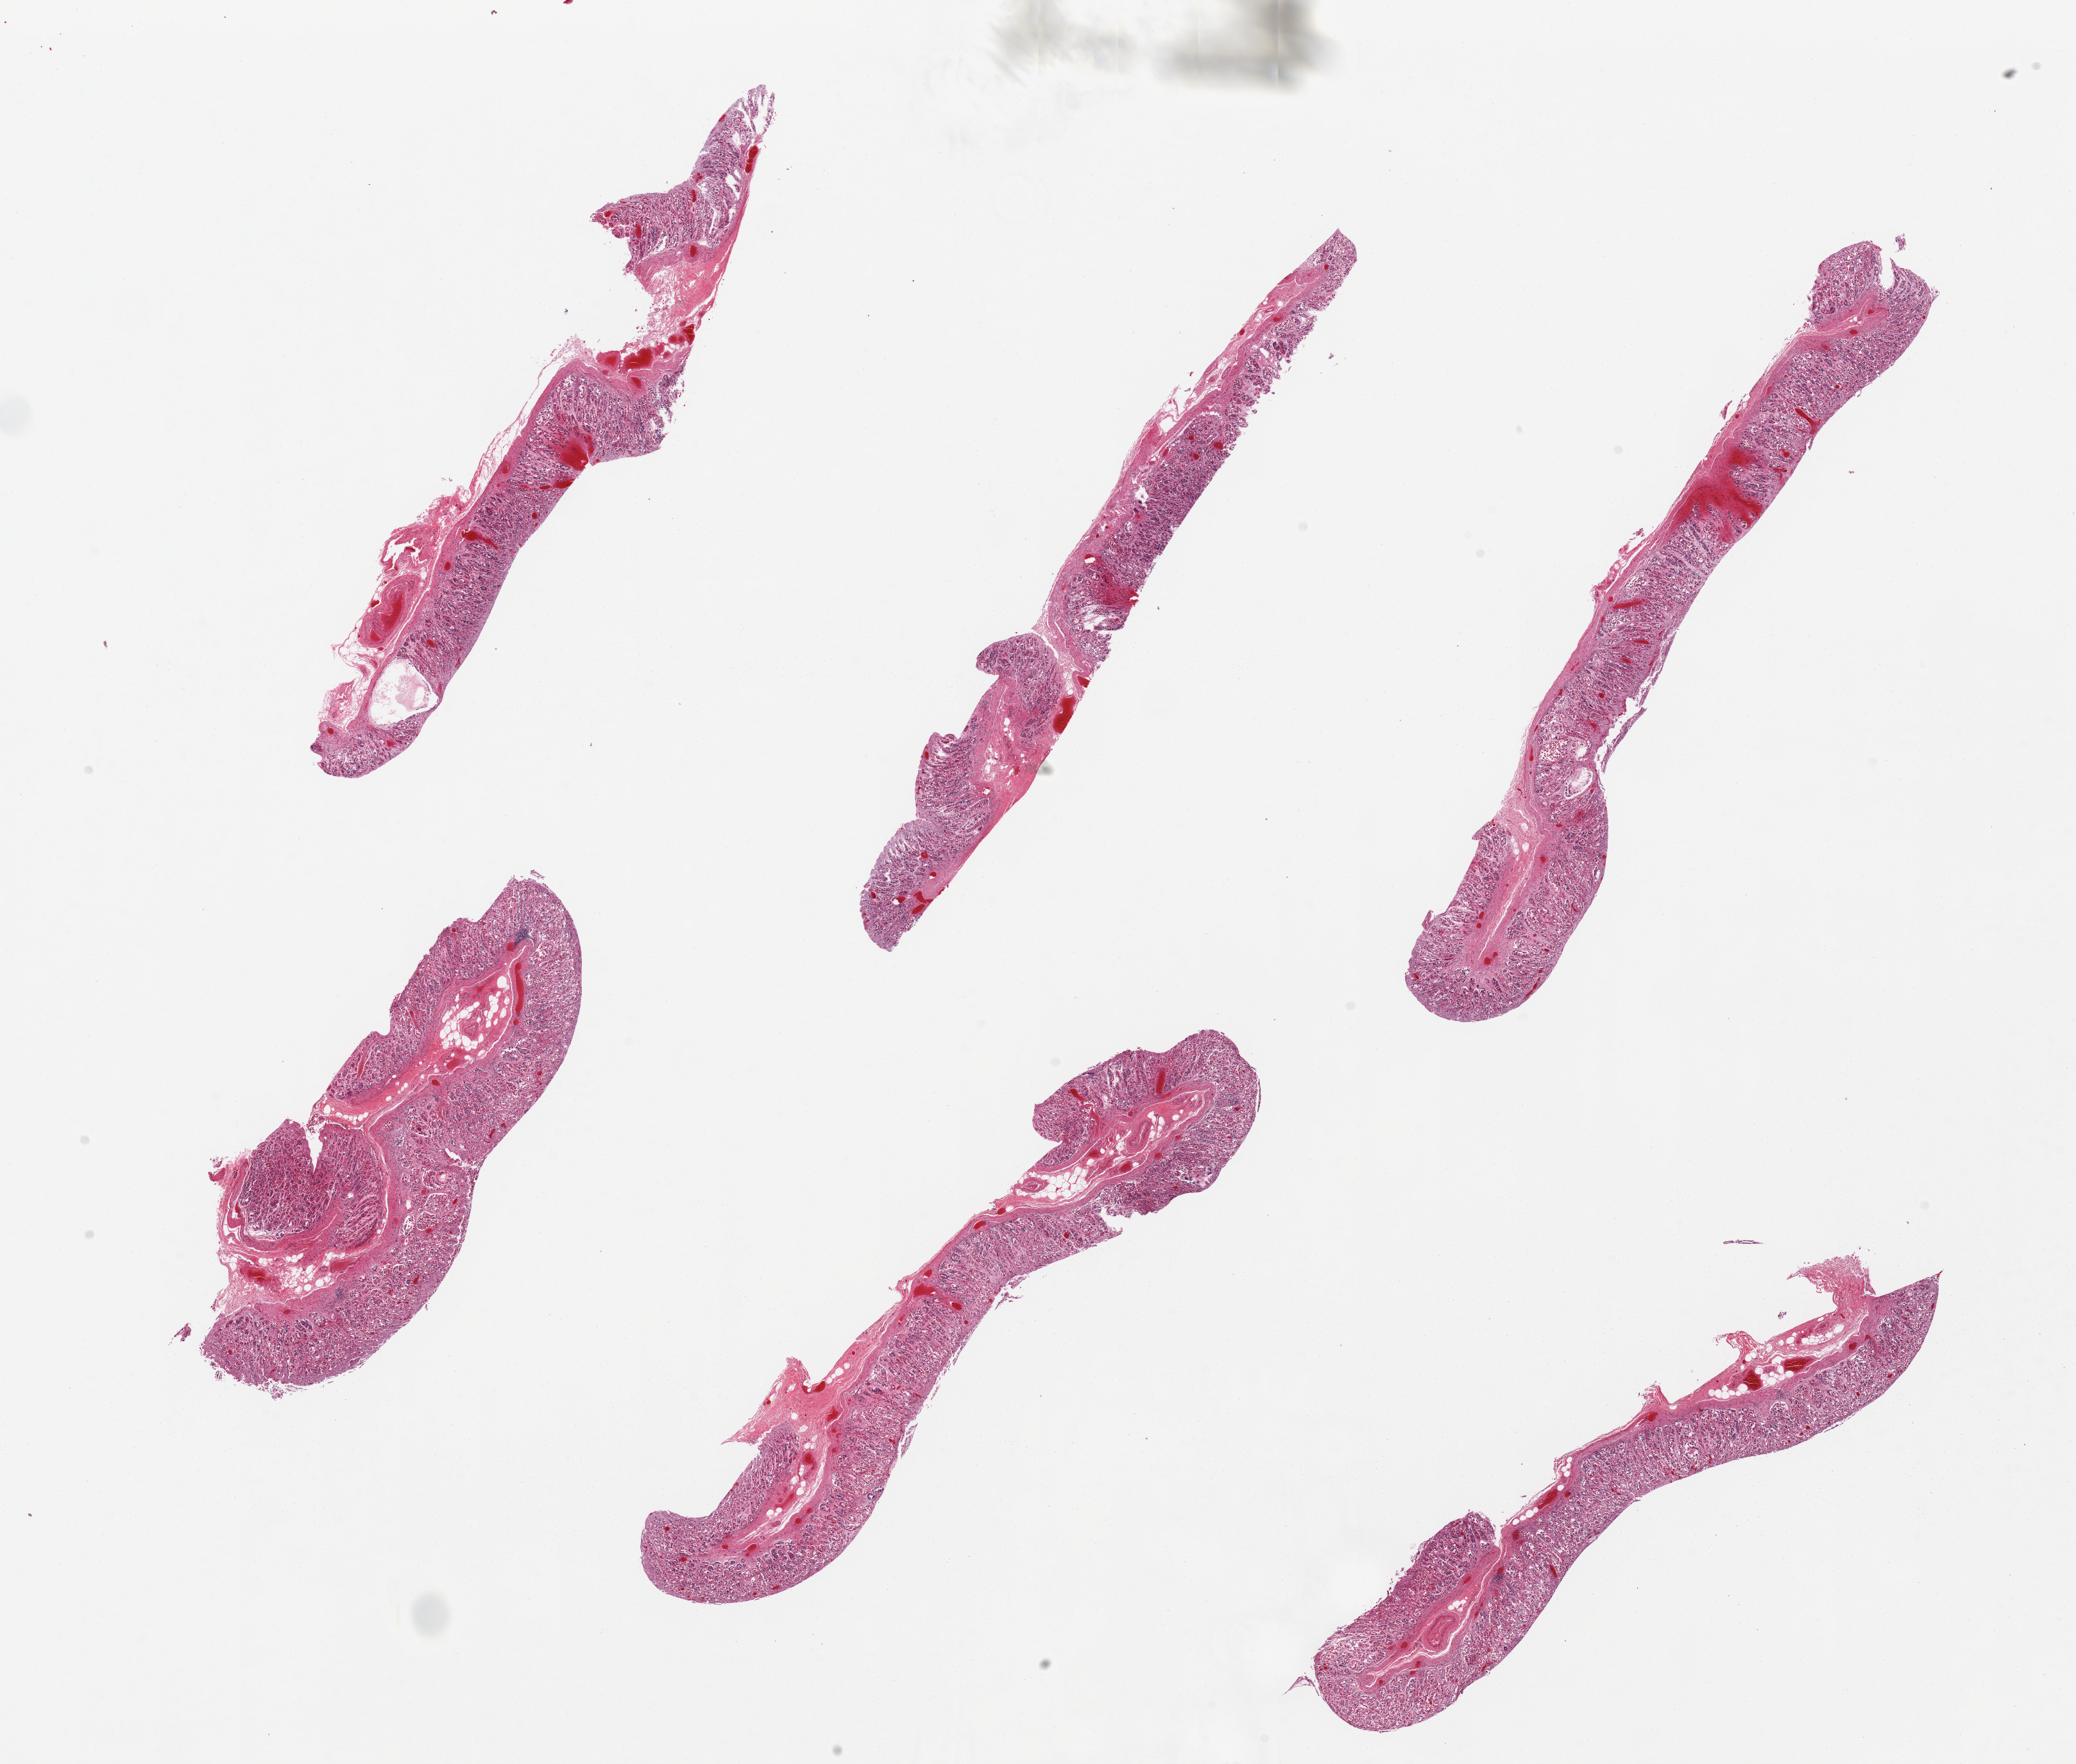
Whole-slide image, hematoxylin and eosin (H&E) stain, brightfield, a low-resolution overview of the entire scanned area, about 25.6 x 21.8 mm. PAXgene-fixed, paraffin-embedded tissue. Sampled site (target tissue): stomach. Tissue donor sample.
* reviewer comment on this tissue sample: 6 pieces